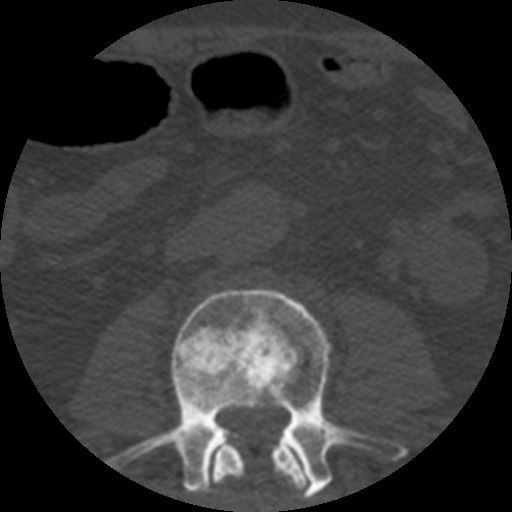
CT including the spine, one axial slice. Bone window (W 1800 / L 400 HU). 1.25 mm slice thickness. 512 × 512 image matrix, field of view 160 × 160 mm. Patient age 57 years. Case-level facts recorded for this patient, not image findings: primary cancer: prostate.
Annotated regions visible in this slice (semi-automatic segmentation, software-assisted and operator-edited):
- L2 vertebra: bounding box [x1, y1, x2, y2] px = [209, 433, 311, 500]
- L3 vertebra: [107, 287, 408, 499]